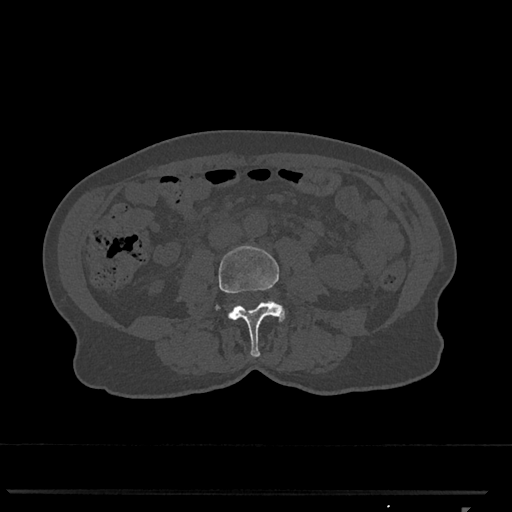
CT including the spine, one axial slice. Slice 264 of 793 in the series (ordered by position). Reconstruction kernel Br40s/3. 120 kVp. Bone window (W 1800 / L 400 HU). 0.5 mm slice thickness. 512 × 512 image matrix. Female patient, age 62 years. Case-level facts recorded for this patient, not image findings: primary cancer: renal.
Outlined on this slice (semi-automatically segmented with operator editing):
- L3 vertebra: bounding box [x1, y1, x2, y2] px = [215, 245, 285, 357]